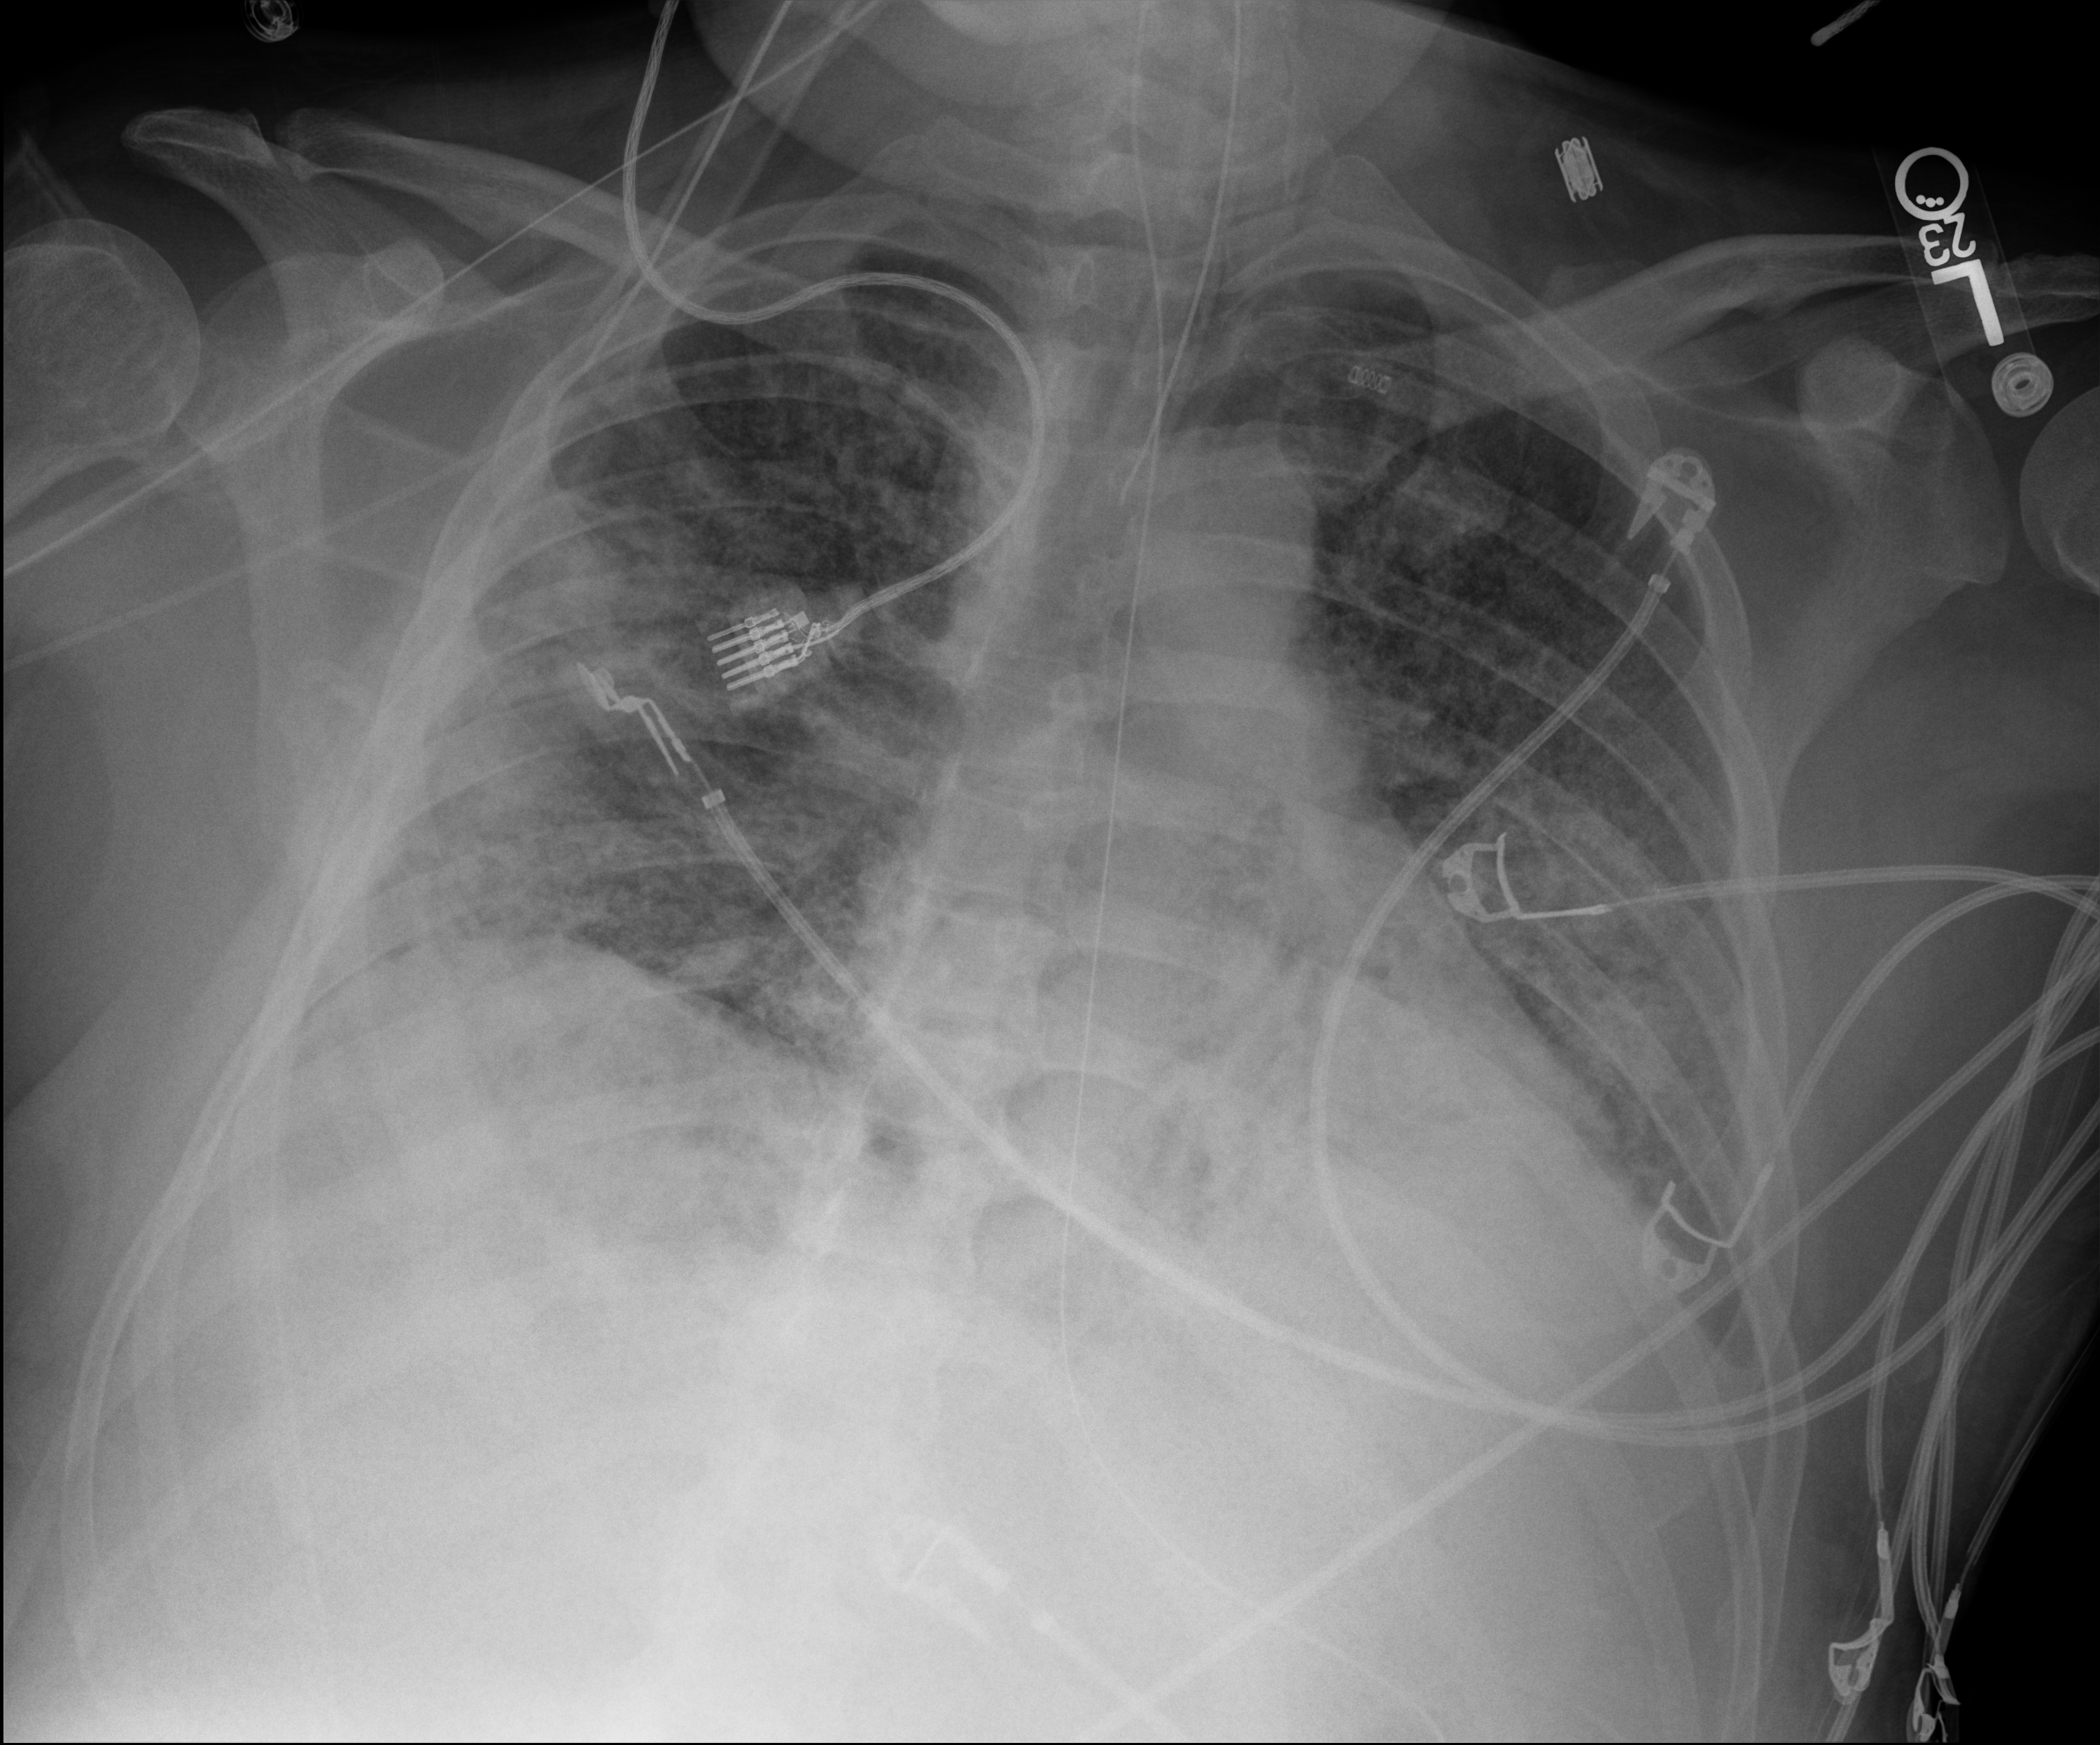
Chest X-ray (portable); anteroposterior (AP) projection. Male patient hospitalised with COVID-19, age 18–59 years.
Admission-level facts for this patient (not findings on this image; timing relative to this image not recorded):
- length of hospital stay: 96 days
- mechanically ventilated during this hospital stay: yes
- admitted to intensive care during this hospital stay: yes